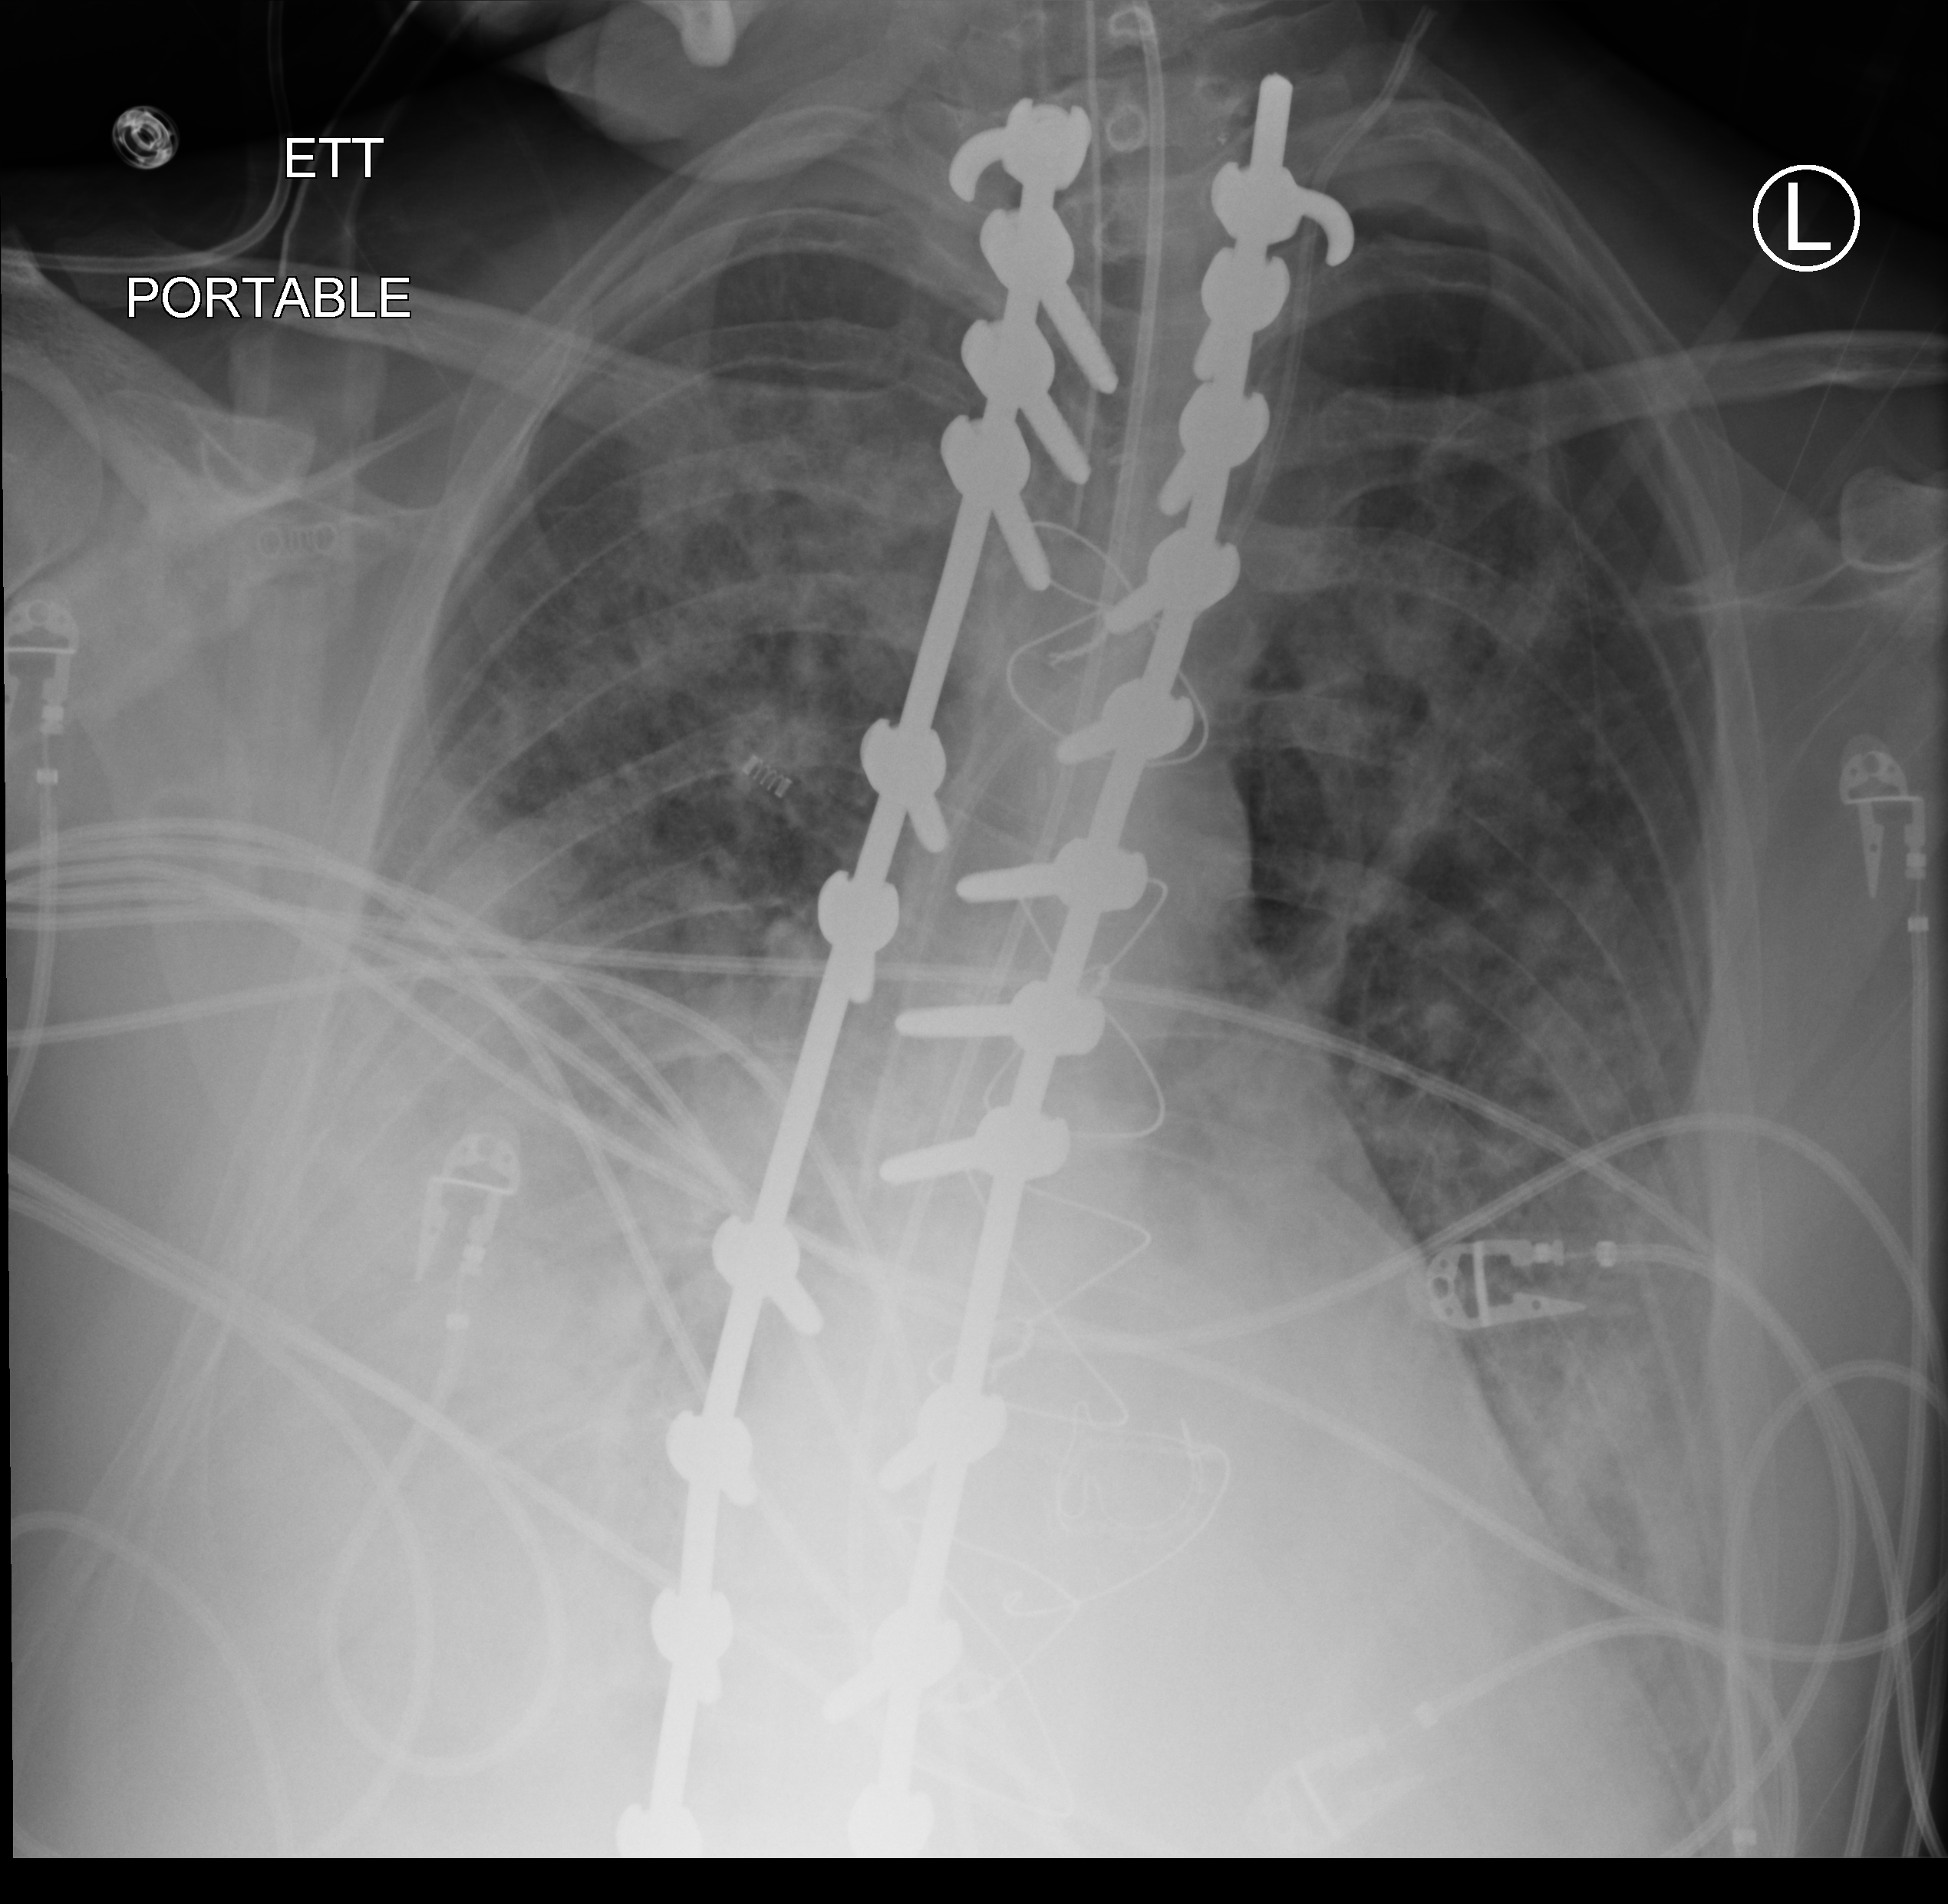
Chest X-ray (portable); anteroposterior (AP) projection. Adult patient hospitalised with COVID-19, age 18–59 years.
Hospital-stay facts (about this admission, not read from this image; timing relative to this image not recorded):
- admitted to intensive care during this hospital stay: yes
- length of hospital stay: 15 days